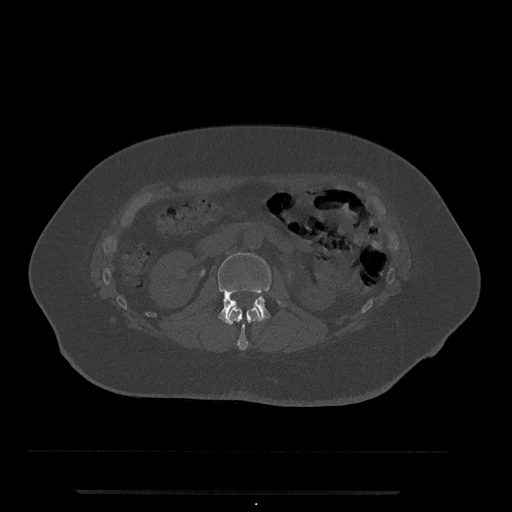
CT including the spine, one axial slice; position 61 of 797 along the scan axis; 120 kVp; bone window (W 1800 / L 400 HU); 0.5 mm slice thickness; 512 × 512 image matrix, field of view 440 × 440 mm. Female patient, age 51 years. From the clinical record (not read from this slice): primary cancer: neuro; vertebrae with lytic lesions (as recorded): T8.
Annotated regions visible in this slice (semi-automatically segmented with operator editing):
- L1 vertebra: bounding box <223,307,261,350> (left, top, right, bottom; pixels)
- L2 vertebra: <218,252,283,322>